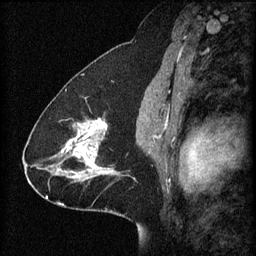
Breast MRI (dynamic contrast-enhanced), one sagittal slice; slice 37 of 60 in the series (ordered by position); 3 images stored at this slice position (order not interpretable as contrast timing); 1.5 T; TE 4.2 ms, TR 8.2 ms; 2 mm slice thickness; 256 × 256 image matrix, field of view 200 × 200 mm. Patient: female, 41 years.
Structures marked on this image (semi-automatic segmentation, software-assisted and operator-edited):
- analysis volume of interest (the breast-tissue region the enhancement analysis was run in; not a lesion): bounding box (x1, y1, x2, y2) in pixels: (58, 118, 122, 181)
- tumour enhancement mask (voxels above the 70 % enhancement threshold inside the analysis volume of interest): (62, 118, 116, 181)